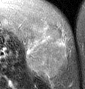
MRI of an extremity soft-tissue mass, one axial slice. Position 16 of 46 along the scan axis. T2-weighted fat-saturated. MR volume resampled by the dataset authors to the PET/CT grid (not the native acquisition matrix). 3.27 mm slice thickness. 85 × 89 image matrix, field of view 83 × 87 mm. Female patient. From the clinical record (not read from this slice): histological type: leiomyosarcoma; grade: intermediate; site of the primary tumour: parascapusular.
Outlined on this slice (expert contour drawn on MRI and transferred to this co-registered scan by the dataset authors):
- gross tumour volume including surrounding oedema: bounding box <27,23,67,79> (left, top, right, bottom; pixels)
- gross tumour volume (mass): <27,23,67,77>